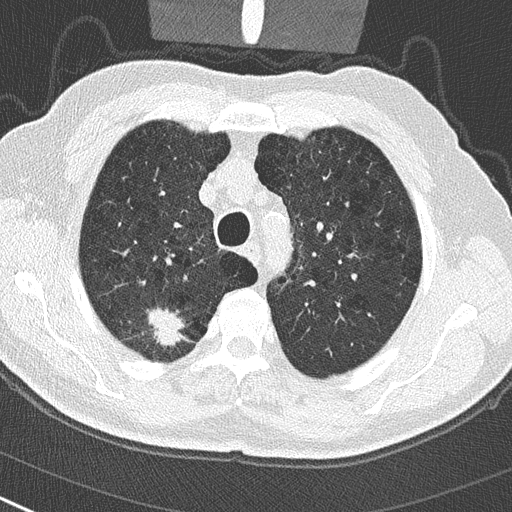
Low-dose screening chest CT, one axial slice; reconstruction kernel B50f; lung window (W 1500 / L -600 HU); 512 × 512 image matrix, field of view 300 × 300 mm.
Annotated regions visible in this slice (expert manual segmentation):
- lesion 1 (tumor, upper lobe of right lung): box from (x=146, y=306) to (x=185, y=349) px